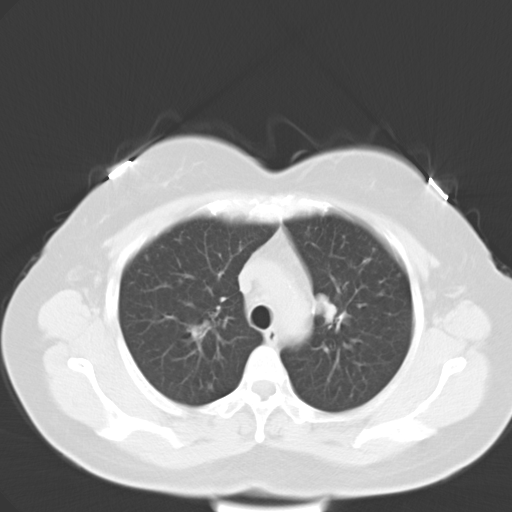
Chest CT, one axial slice; lung window (W 1500 / L -600 HU); 512 × 512 image matrix, field of view 353 × 353 mm. Patient: female, 53 years. From the clinical record (not read from this slice): clinical TNM (as recorded): T1c N0 M1a.
Outlined on this slice (bounding box drawn by a radiologist):
- lung tumour (recorded histology: adenocarcinoma): bounding box [x1, y1, x2, y2] px = [312, 292, 339, 327]